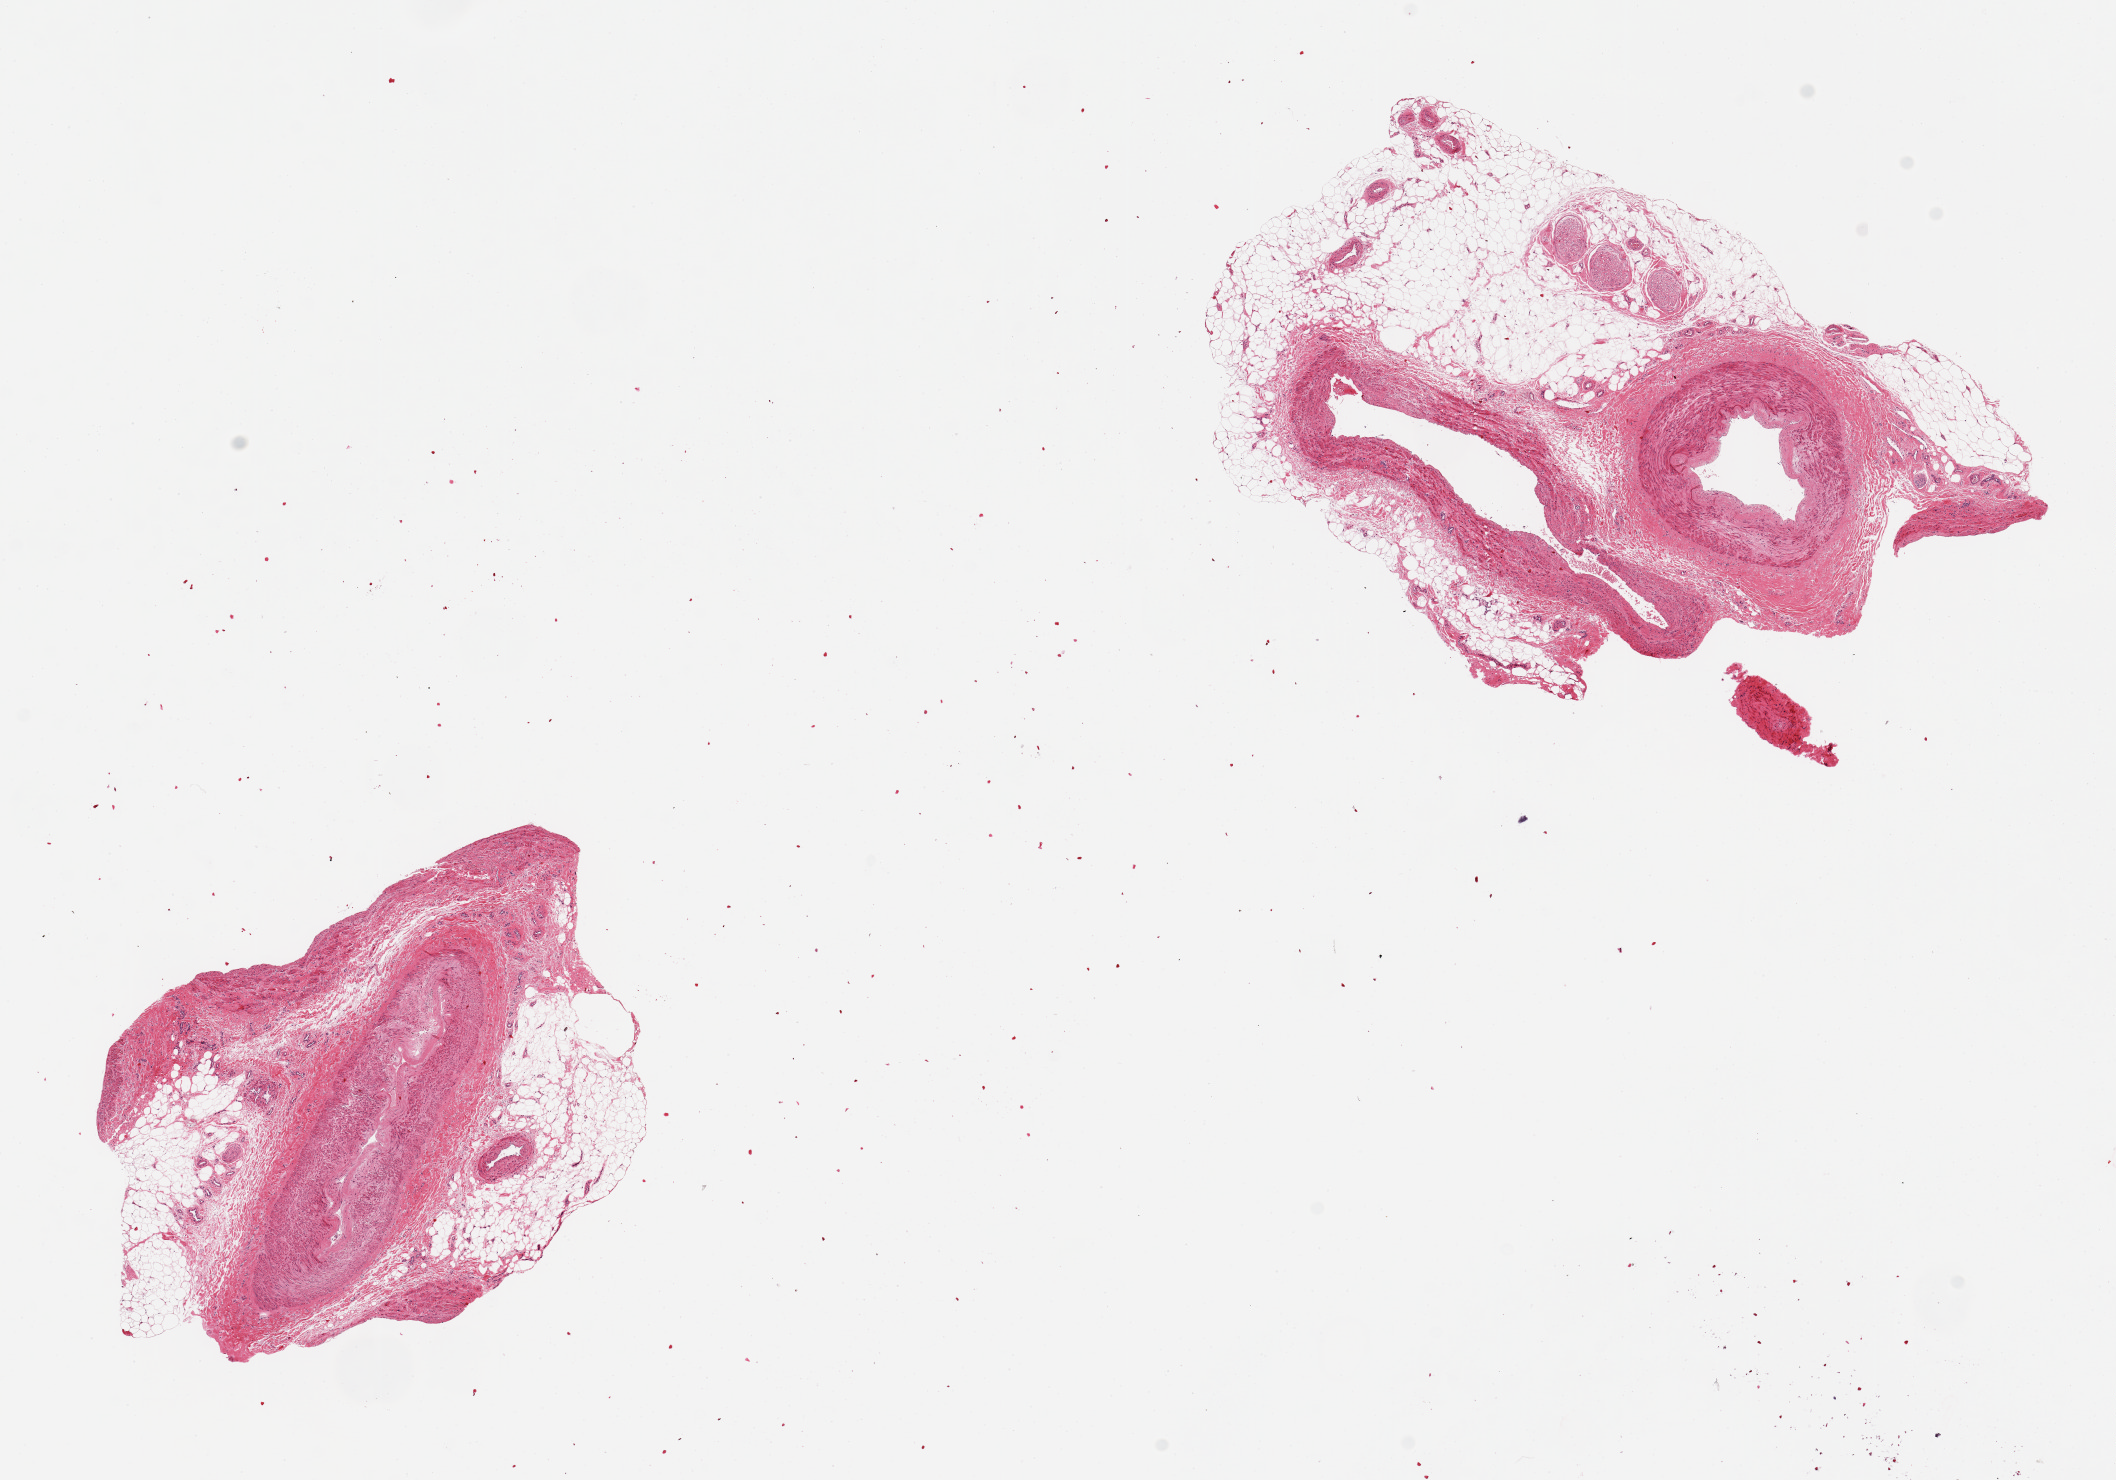
Haematoxylin and eosin whole-slide image, brightfield — a low-resolution overview of the entire scanned area, about 16.7 x 11.7 mm, PAXgene-fixed paraffin-embedded (PFPE) section, section of tibial artery (target tissue), tissue donor sample.
Pathologist's review note for this sample: 2 pieces, adherent rims of fat/peripheral nerve, ~1.5-2mm.